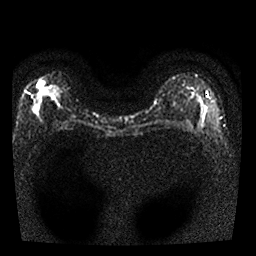
Breast MRI, one axial slice. Slice 15 of 25 in the series (ordered by position). Diffusion-weighted series; image 2 of 4 stored at this slice position (different b-values; order by instance number). 1.5 T. 4 mm slice thickness. 256 × 256 image matrix, field of view 300 × 300 mm. Female patient.
Outlined on this slice (expert manual segmentation):
- tumour on diffusion-weighted imaging: box from (x=36, y=80) to (x=47, y=96) px